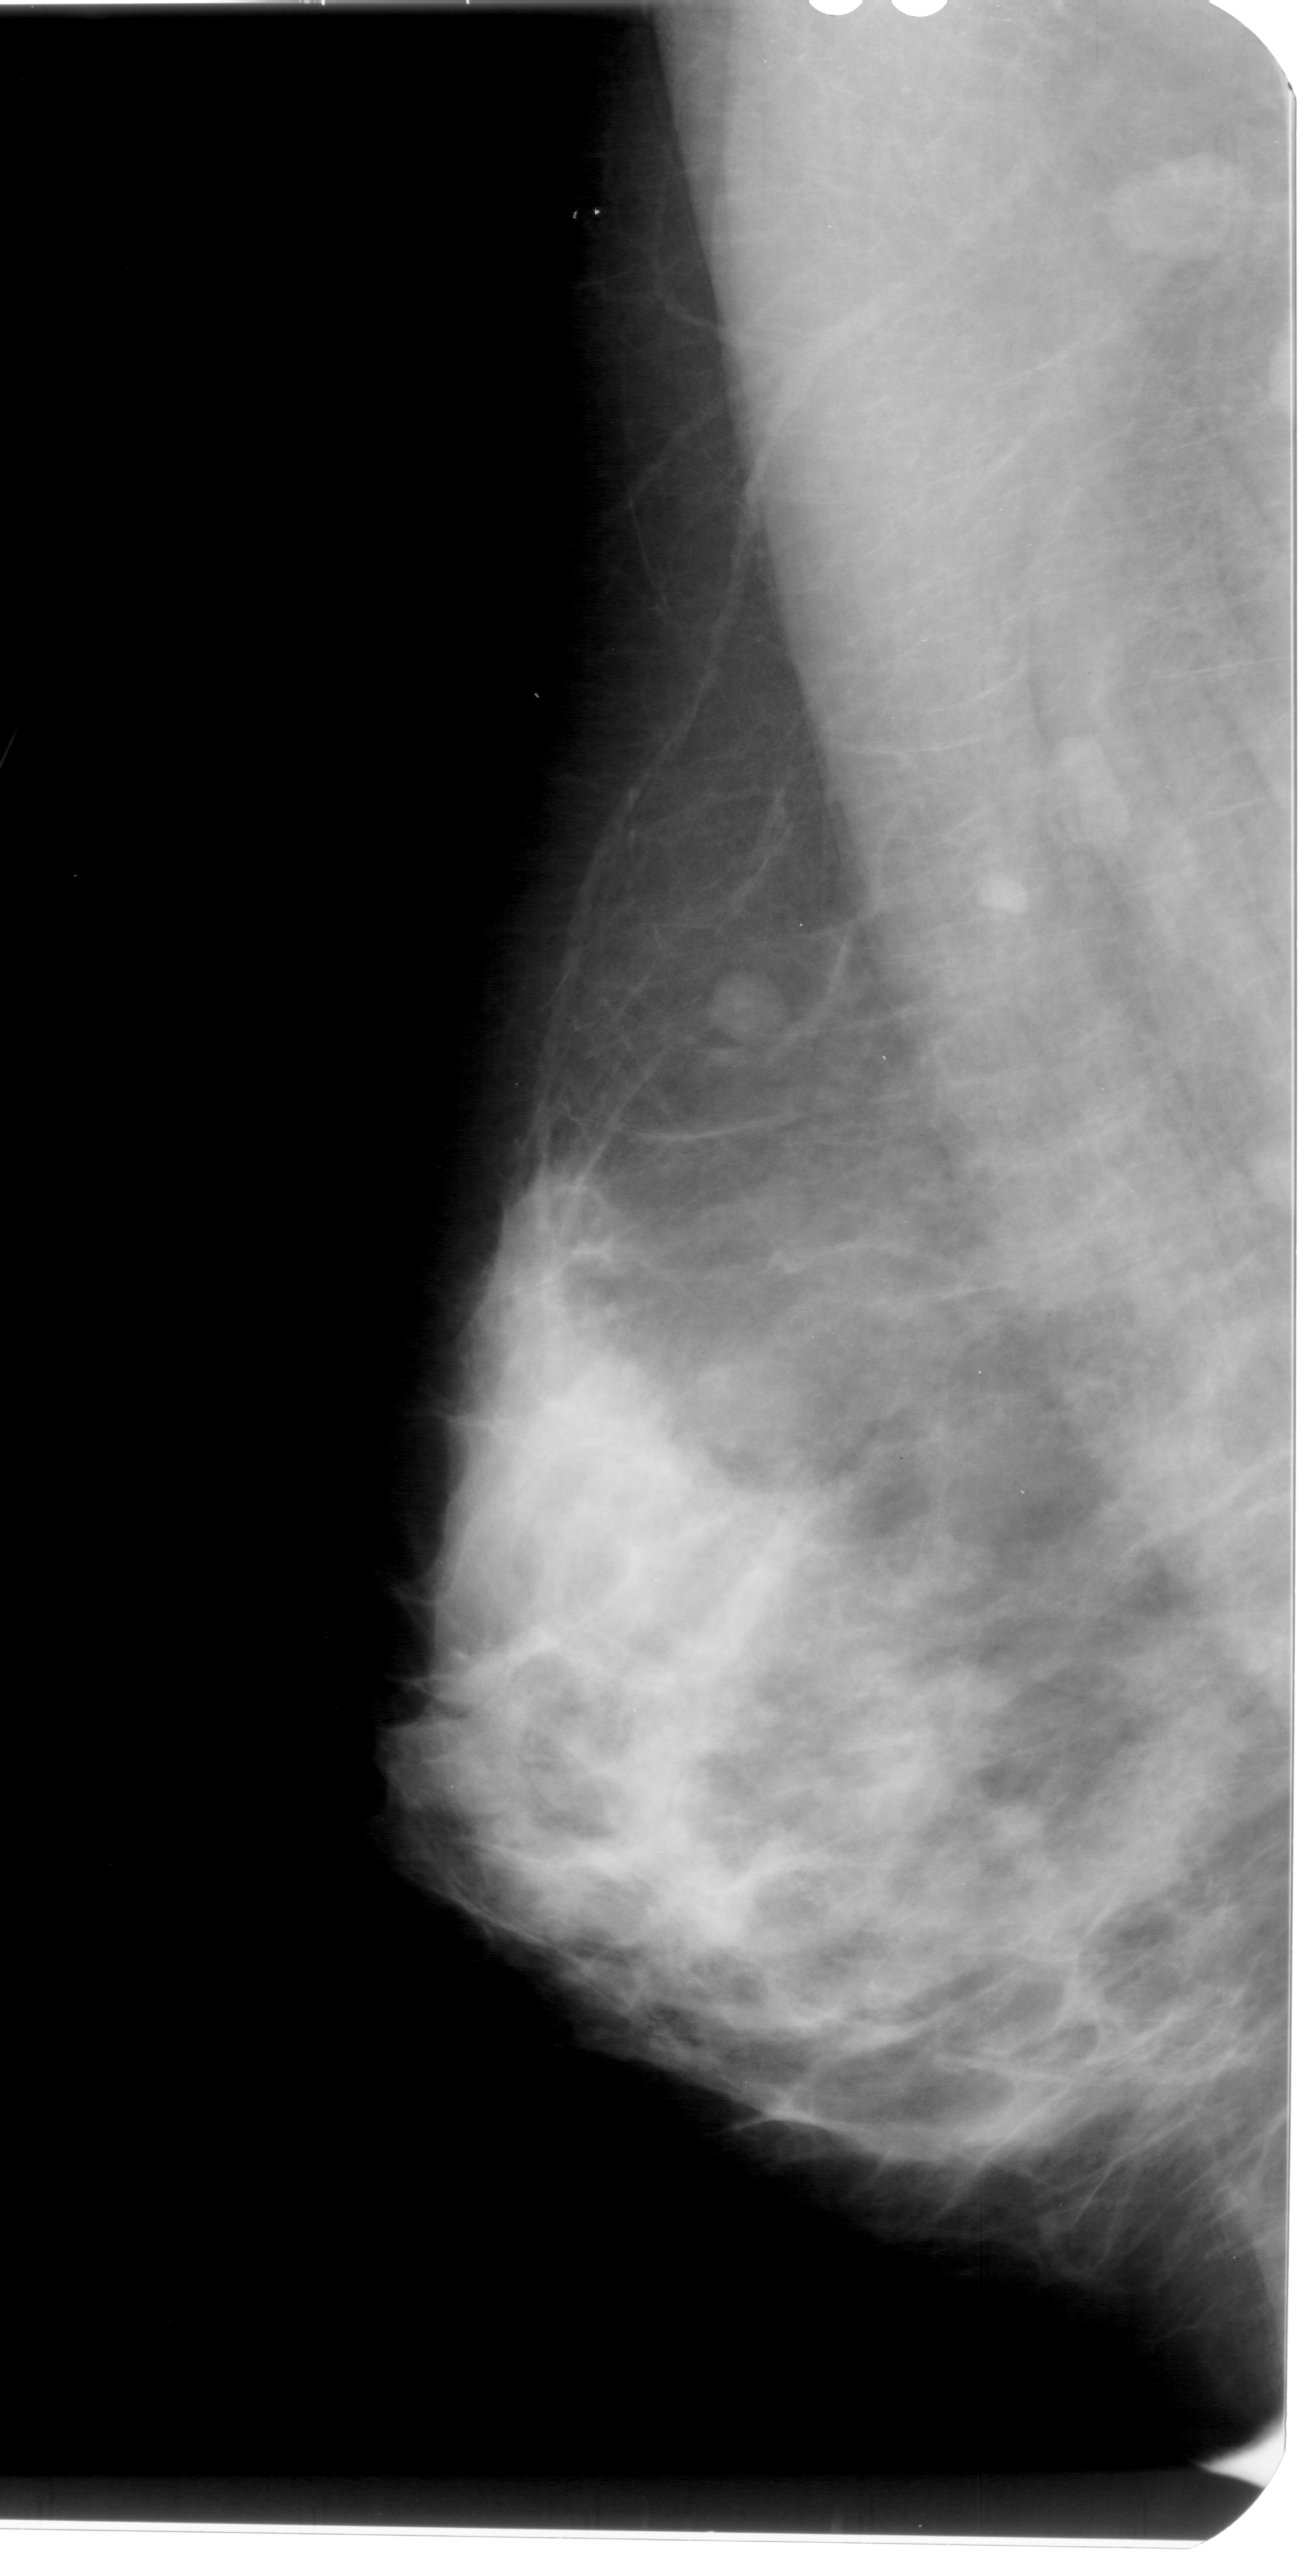
Mammogram (digitized film); left breast; mediolateral oblique (MLO) view; BI-RADS breast density category 4 (scale 1–4).
Calcifications, morphology amorphous, distribution clustered; BI-RADS assessment category 4; pathology result (as recorded, not read from the image): benign.